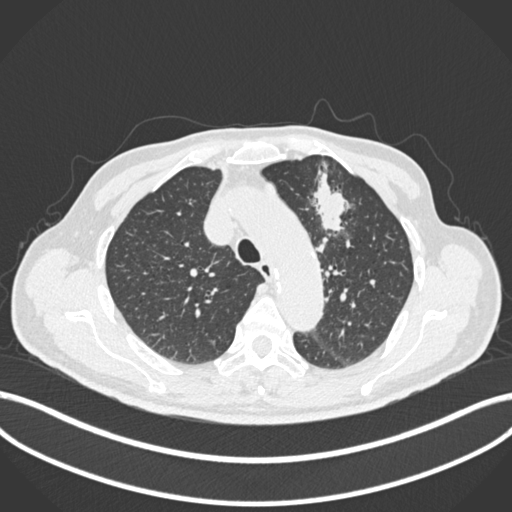
Chest CT, one axial slice; position 188 of 261 along the scan axis; 120 kVp; lung window (W 1500 / L -600 HU); 512 × 512 image matrix, field of view 400 × 400 mm. Male patient, age 74 years. From the clinical record (not read from this slice): clinical TNM (as recorded): T2b N0 M1c.
Annotated regions visible in this slice (rectangle marked by the reading radiologist):
- lung tumour (recorded histology: adenocarcinoma): bounding box <310,167,355,239> (left, top, right, bottom; pixels)